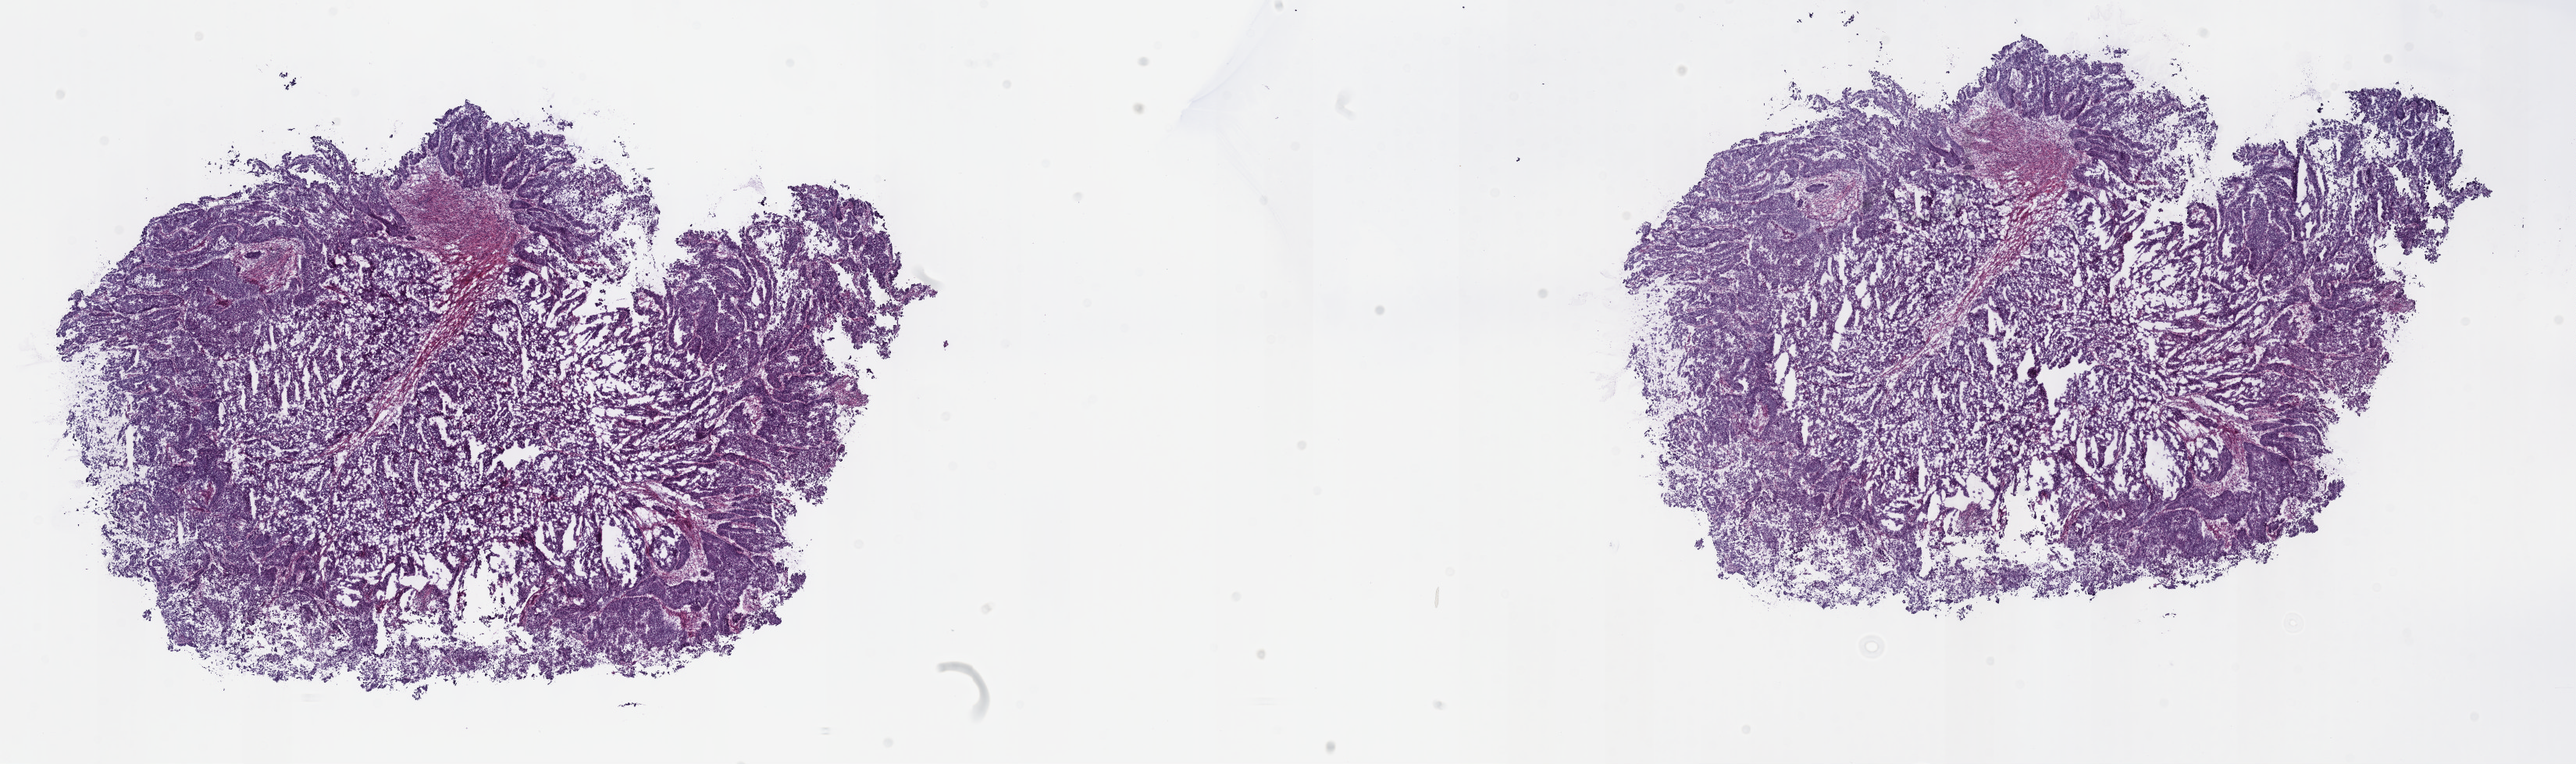
Hematoxylin and eosin (H&E) stained whole-slide image — a low-resolution overview of the entire scanned area, about 26.7 x 7.9 mm, frozen section from the top of the tissue portion, primary tumour sample from the uterus. Patient: female, age at initial diagnosis 69 years. Histologic grade: G2 (moderately differentiated). Slide review estimates, as recorded: tumour cells 80%, tumour nuclei 80%, normal cells 0%, stromal cells 10%, necrosis 10%. Infiltration values recorded for this section: lymphocyte infiltration 60%, monocyte infiltration 20%, neutrophil infiltration 20%.
Diagnosis: Endometrioid adenocarcinoma, NOS (endometrium). FIGO stage: IA. Lymph nodes positive (case pathology): 0 of 42 examined.